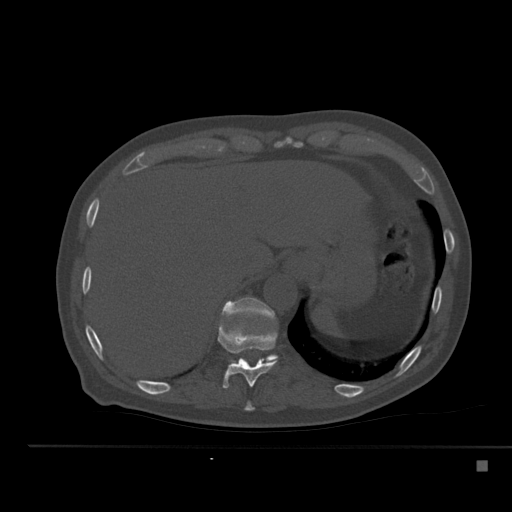
CT including the spine, one axial slice. Position 265 of 517 along the scan axis. Reconstruction kernel Br40s. 120 kVp. Bone window (W 1800 / L 400 HU). 1.5 mm slice thickness. 512 × 512 image matrix, field of view 408 × 408 mm. Patient: male, 70 years. From the clinical record (not read from this slice): primary cancer: renal; vertebrae with lytic lesions (as recorded): T4, T6, T10, T12, L3, L4, L5.
Outlined on this slice (semi-automatically segmented with operator editing):
- T10 vertebra: box from (x=217, y=320) to (x=277, y=389) px
- T11 vertebra: (x=221, y=297)–(x=278, y=361)
- T9 vertebra: (x=244, y=401)–(x=254, y=411)